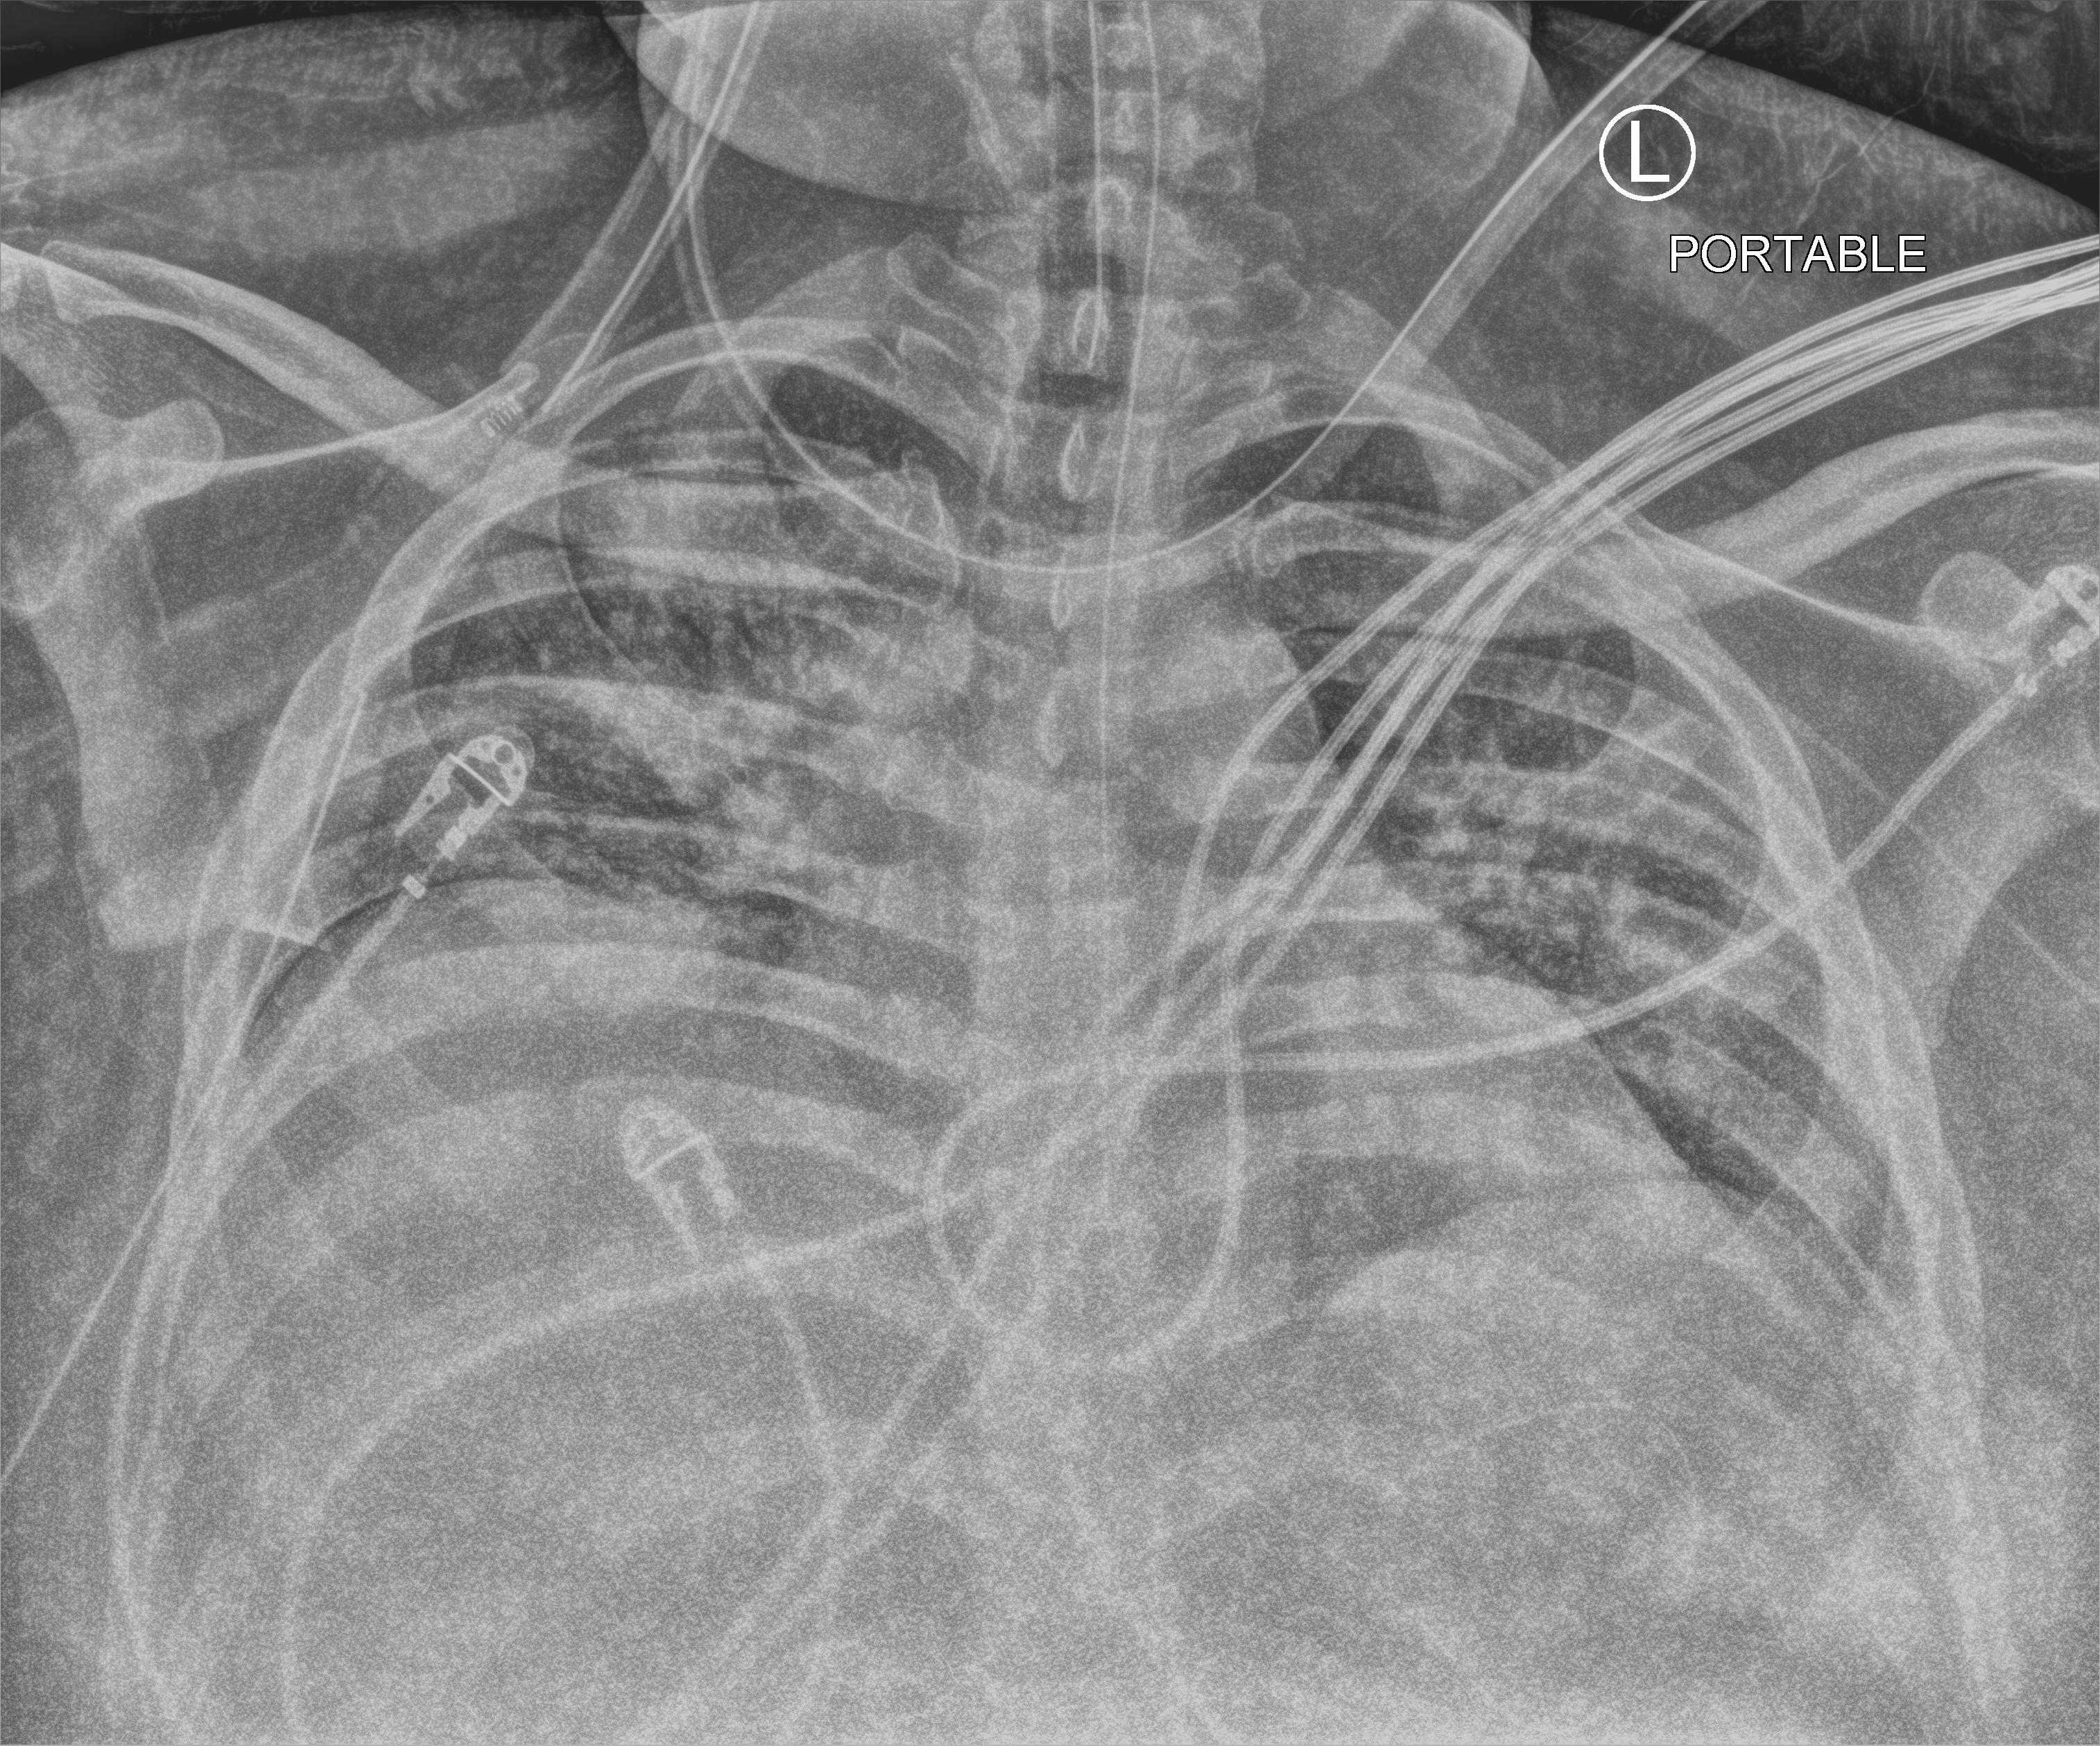
Portable chest radiograph. Male patient hospitalised with COVID-19, age 18–59 years.
Hospital-stay facts (about this admission, not read from this image; timing relative to this image not recorded):
- admitted to intensive care during this hospital stay: yes
- length of hospital stay: 69 days
- other chronic lung disease (admission record): yes